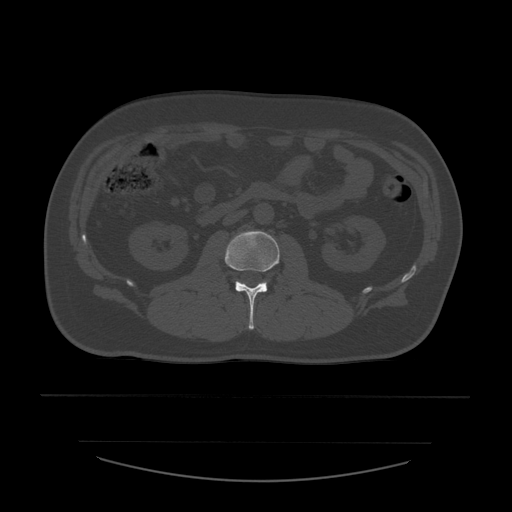
CT including the spine, one axial slice. Slice 195 of 532 in the series (ordered by position). 120 kVp. Bone window (W 1800 / L 400 HU). 1.25 mm slice thickness. 512 × 512 image matrix. Patient age 44 years. Case-level facts recorded for this patient, not image findings: primary cancer: soft tissue sarcoma.
Annotated regions visible in this slice (semi-automatically segmented with operator editing):
- L2 vertebra: bounding box <225,231,280,330> (left, top, right, bottom; pixels)